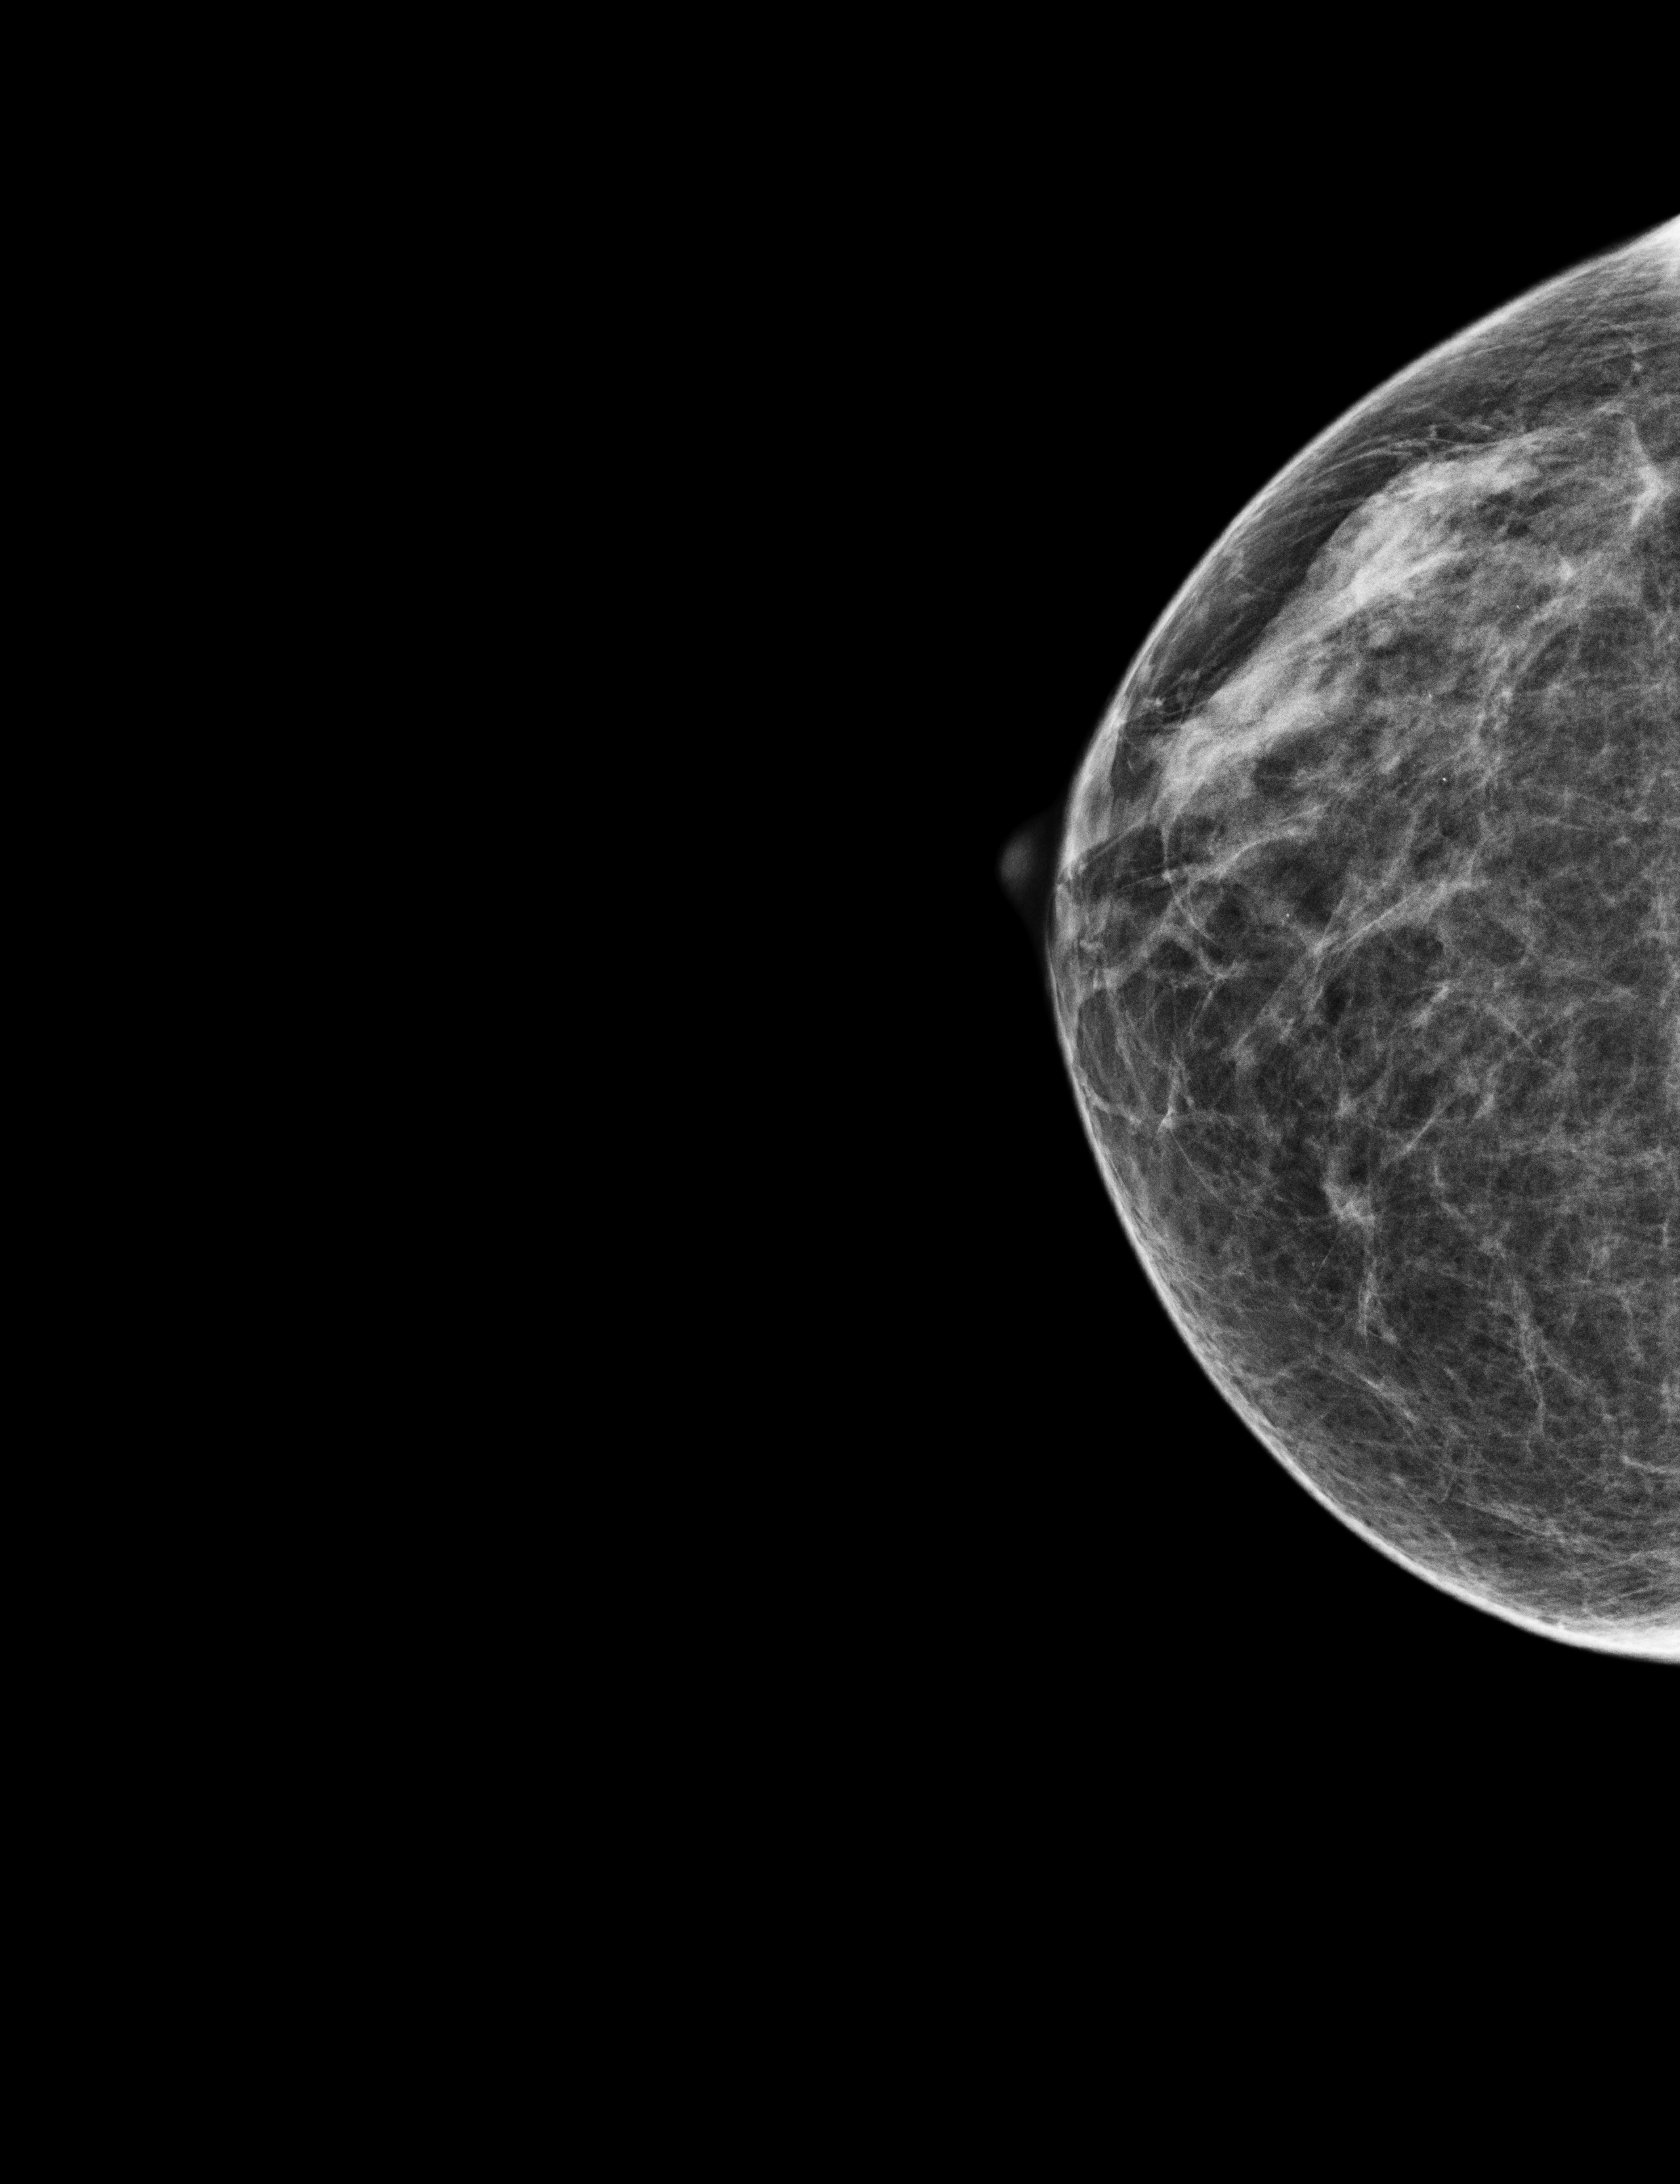
Annual screening mammography examination. Patient: female, 68 years.
Image type: full-field digital mammogram. Breast: right. Projection: cranio-caudal projection.